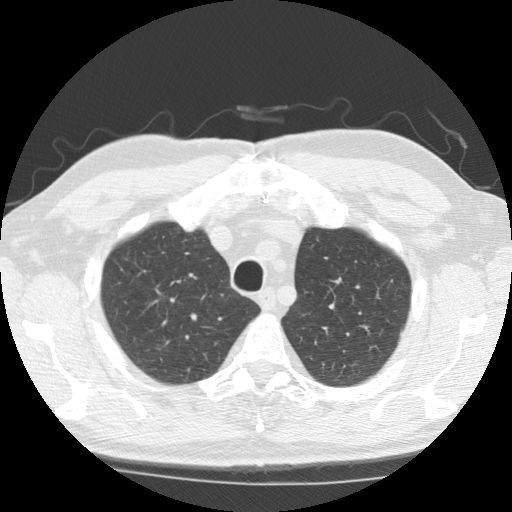
Low-dose screening chest CT, one axial slice. Position 156 of 196 along the scan axis. 120 kVp. Lung window (W 1500 / L -600 HU). 2.5 mm slice thickness. 512 × 512 image matrix, field of view 350 × 350 mm.
Structures marked on this image (outlined manually by an expert reader):
- lesion 1 (tumor, upper lobe of right lung): box from (x=151, y=337) to (x=174, y=357) px